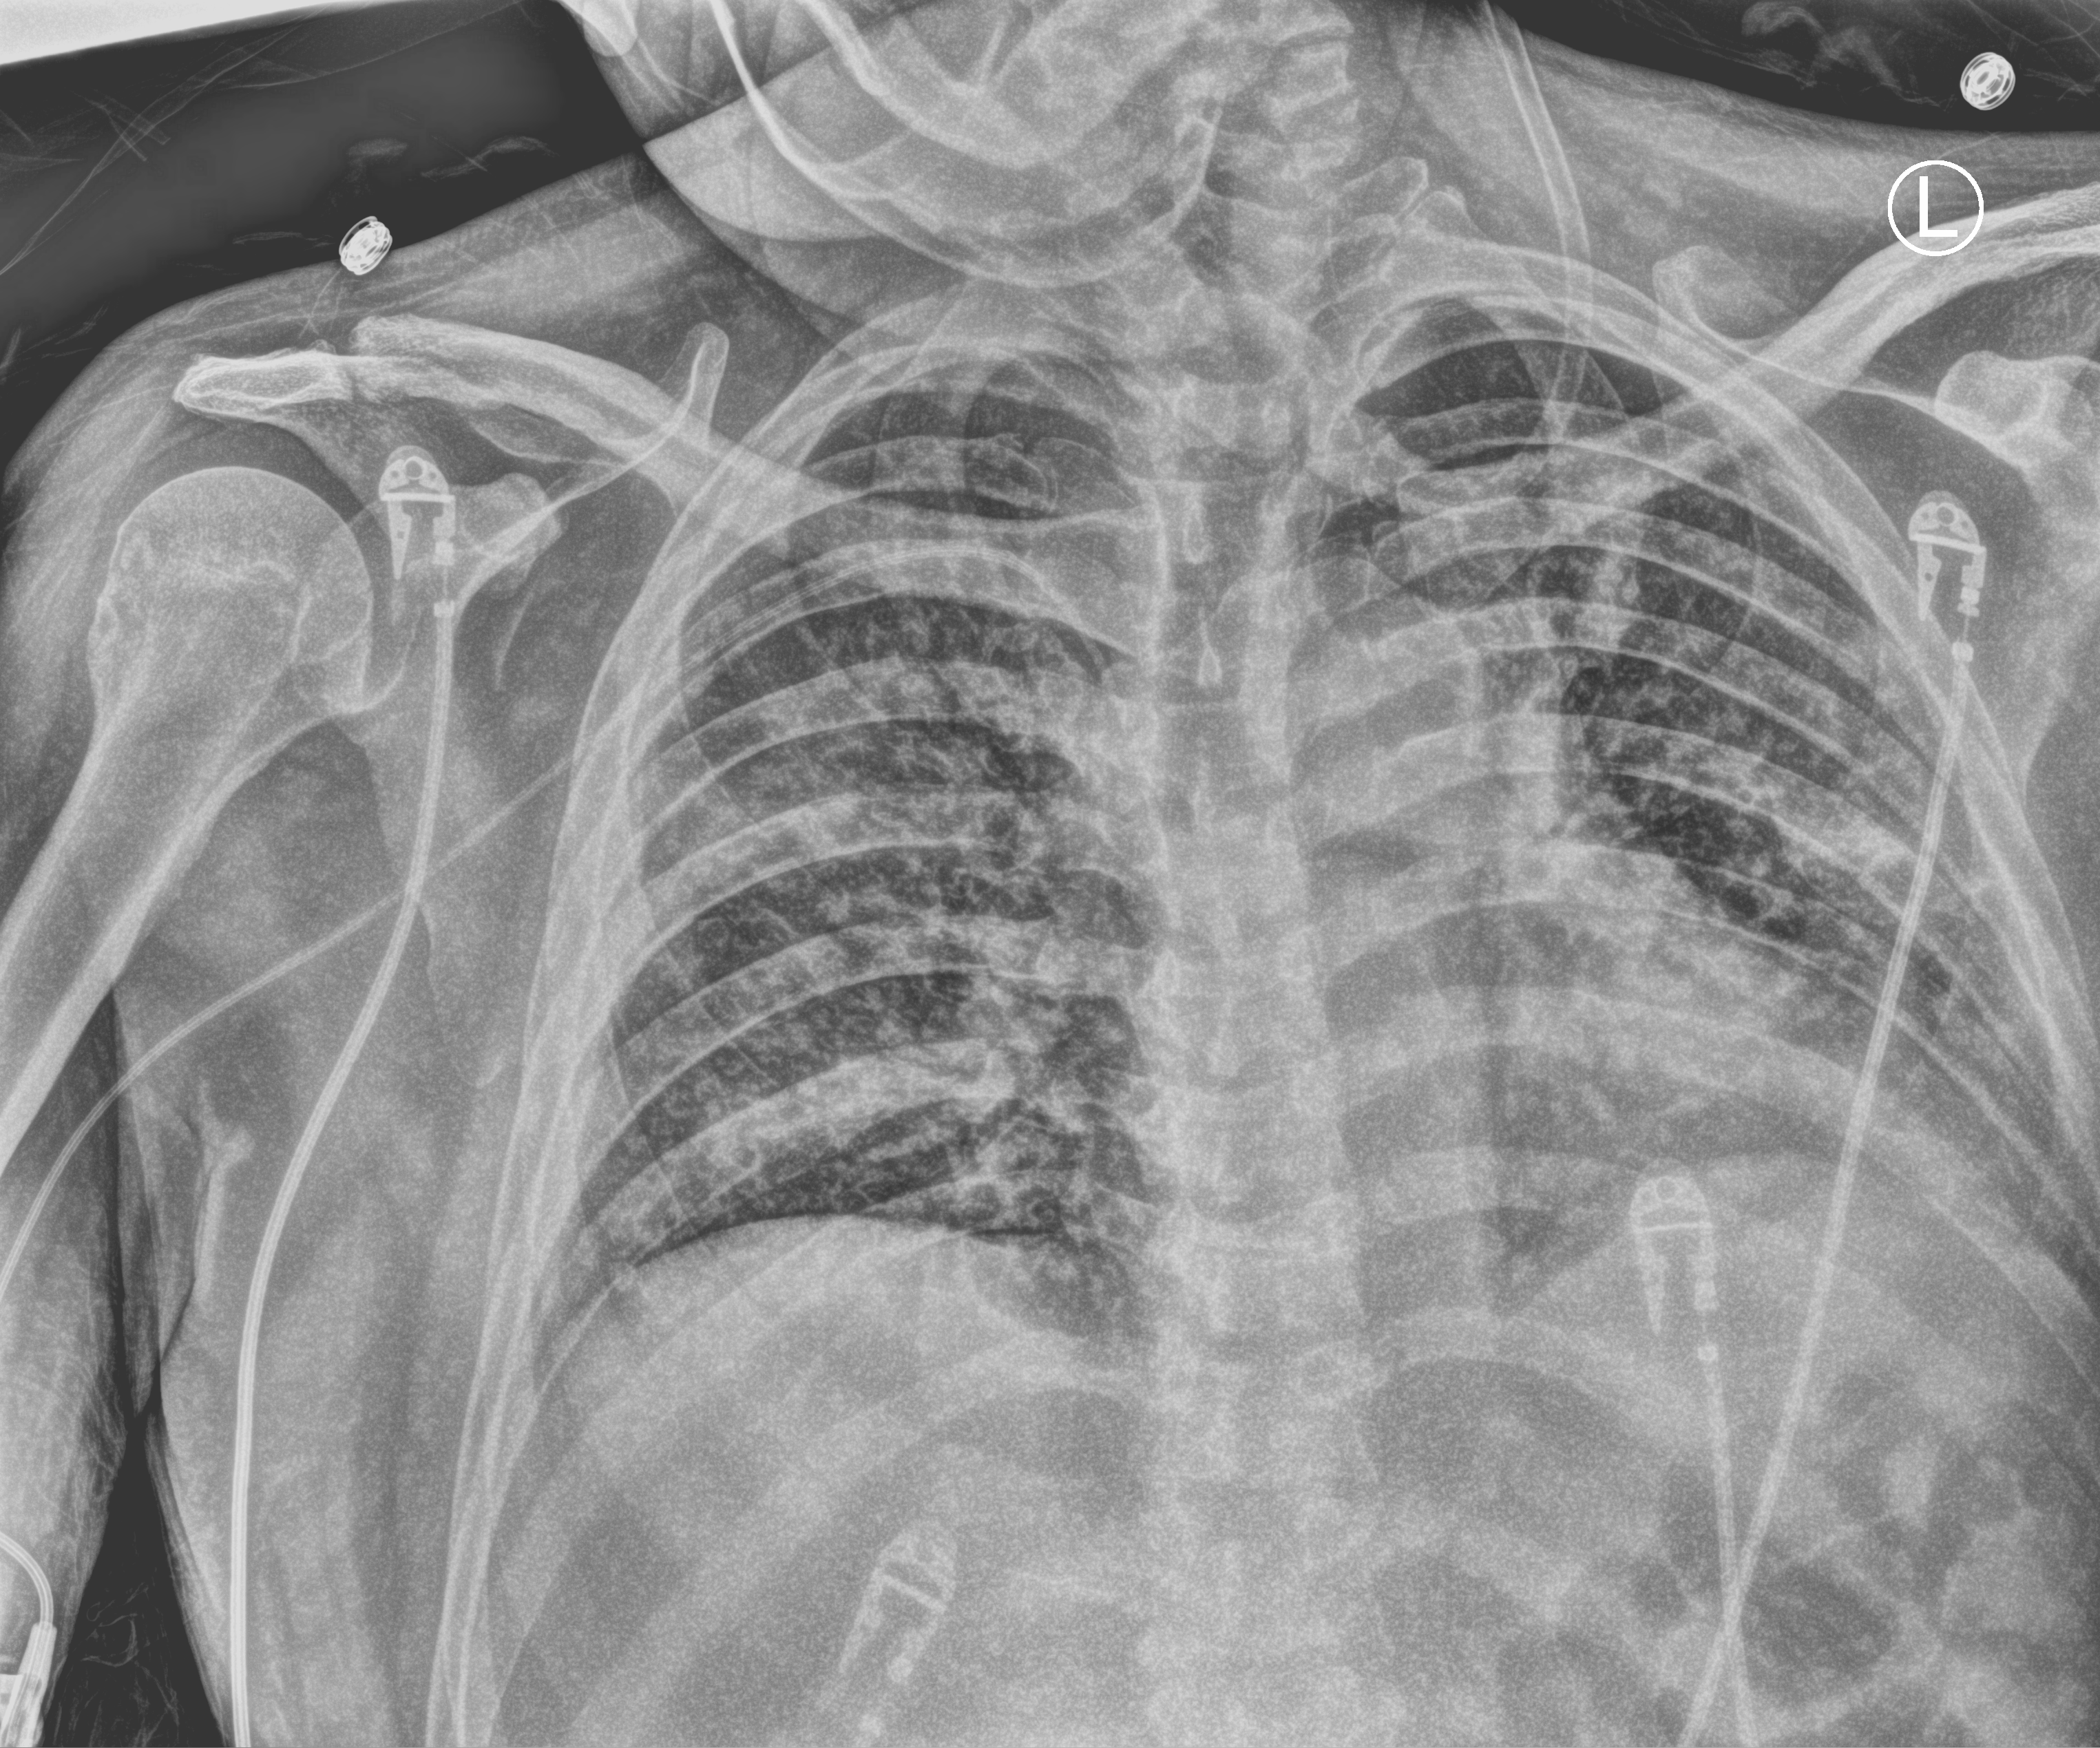
Portable chest radiograph, anteroposterior (AP) projection. Patient hospitalised with COVID-19; male, aged 18–59 years.
From the hospital-stay record, not from the radiograph (when in the stay this image was taken is not recorded): mechanically ventilated during this hospital stay: yes; admitted to intensive care during this hospital stay: yes; other chronic lung disease (admission record): no.